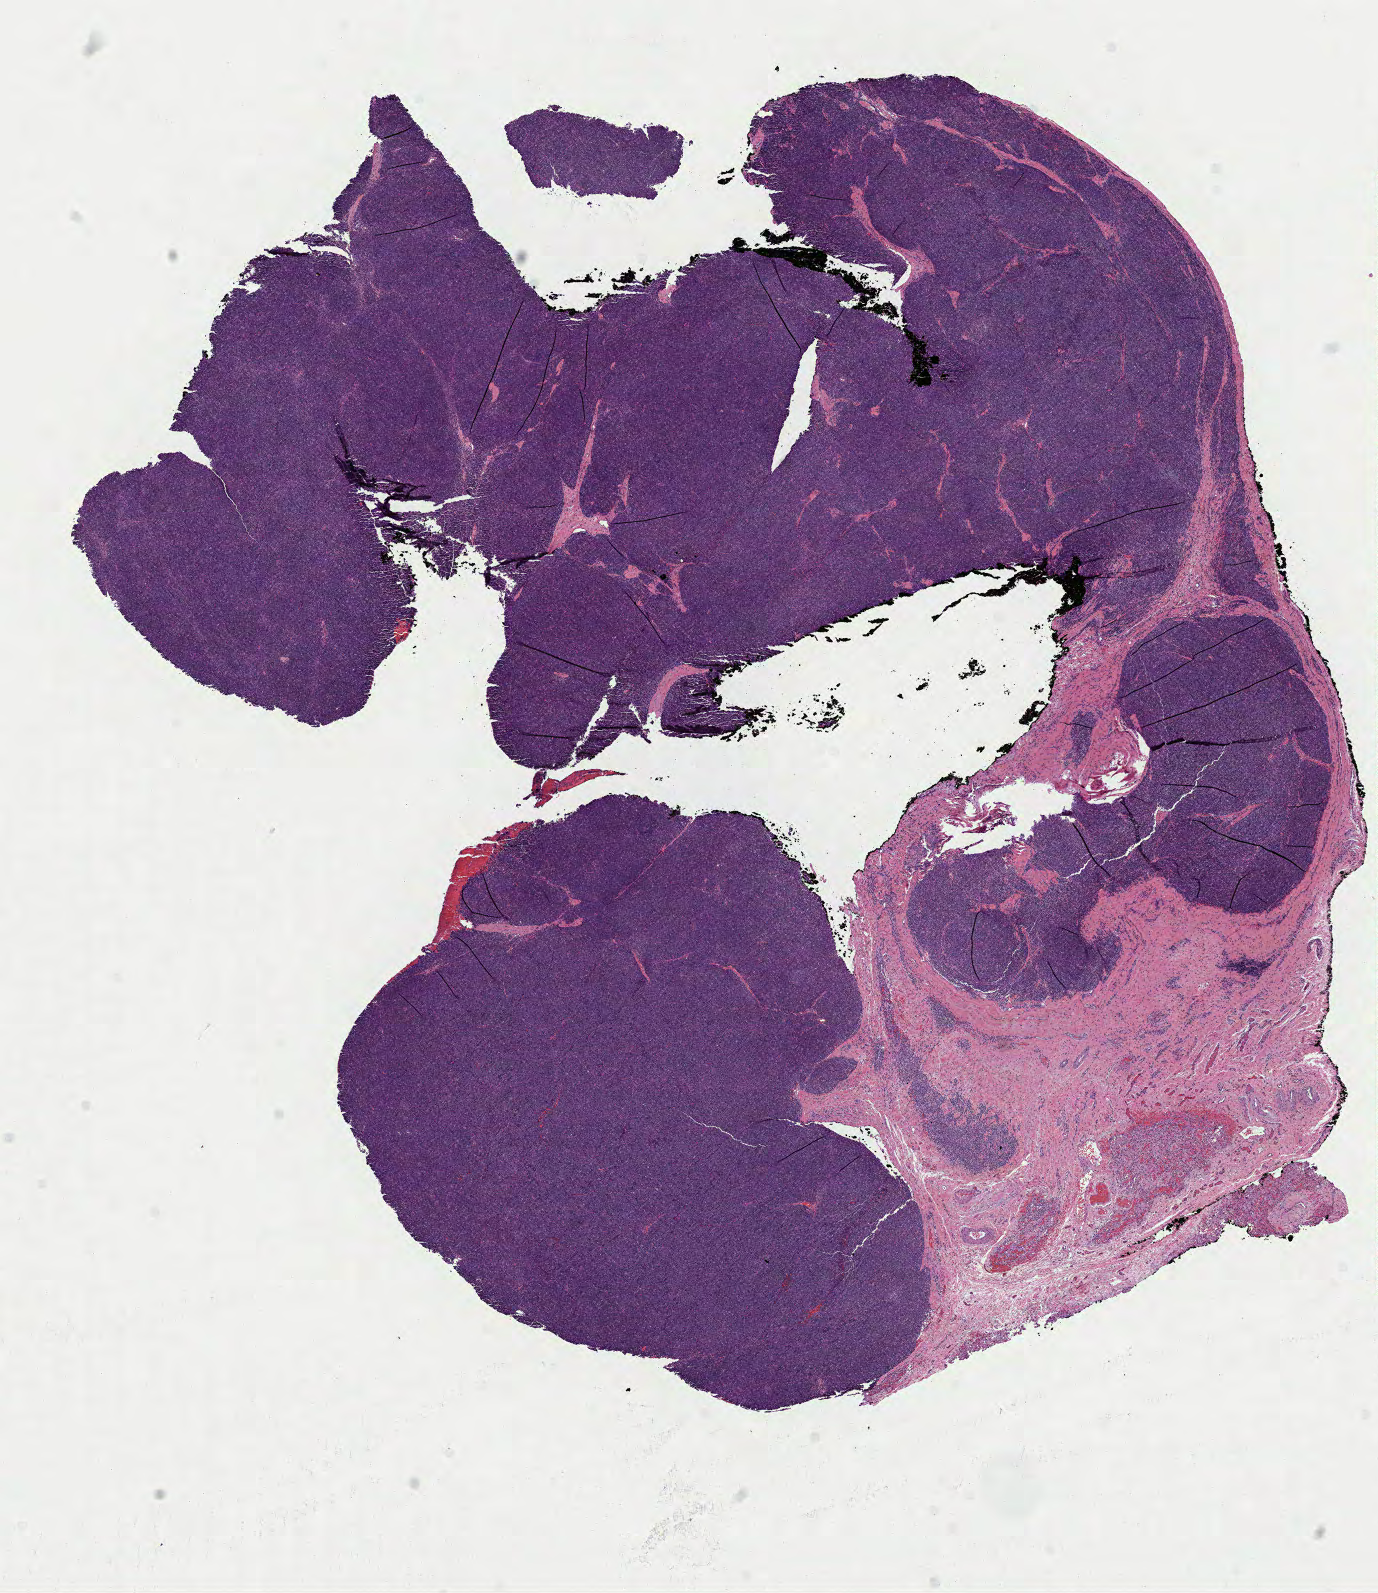
Hematoxylin and eosin (H&E) stained whole-slide image — low-resolution overview of the scanned area, about 11.1 x 12.9 mm. FFPE section. Primary tumour sample from the thymus. Female patient; age at initial diagnosis 73 years.
Histologic diagnosis: Thymoma, type A, NOS (thorax, NOS).